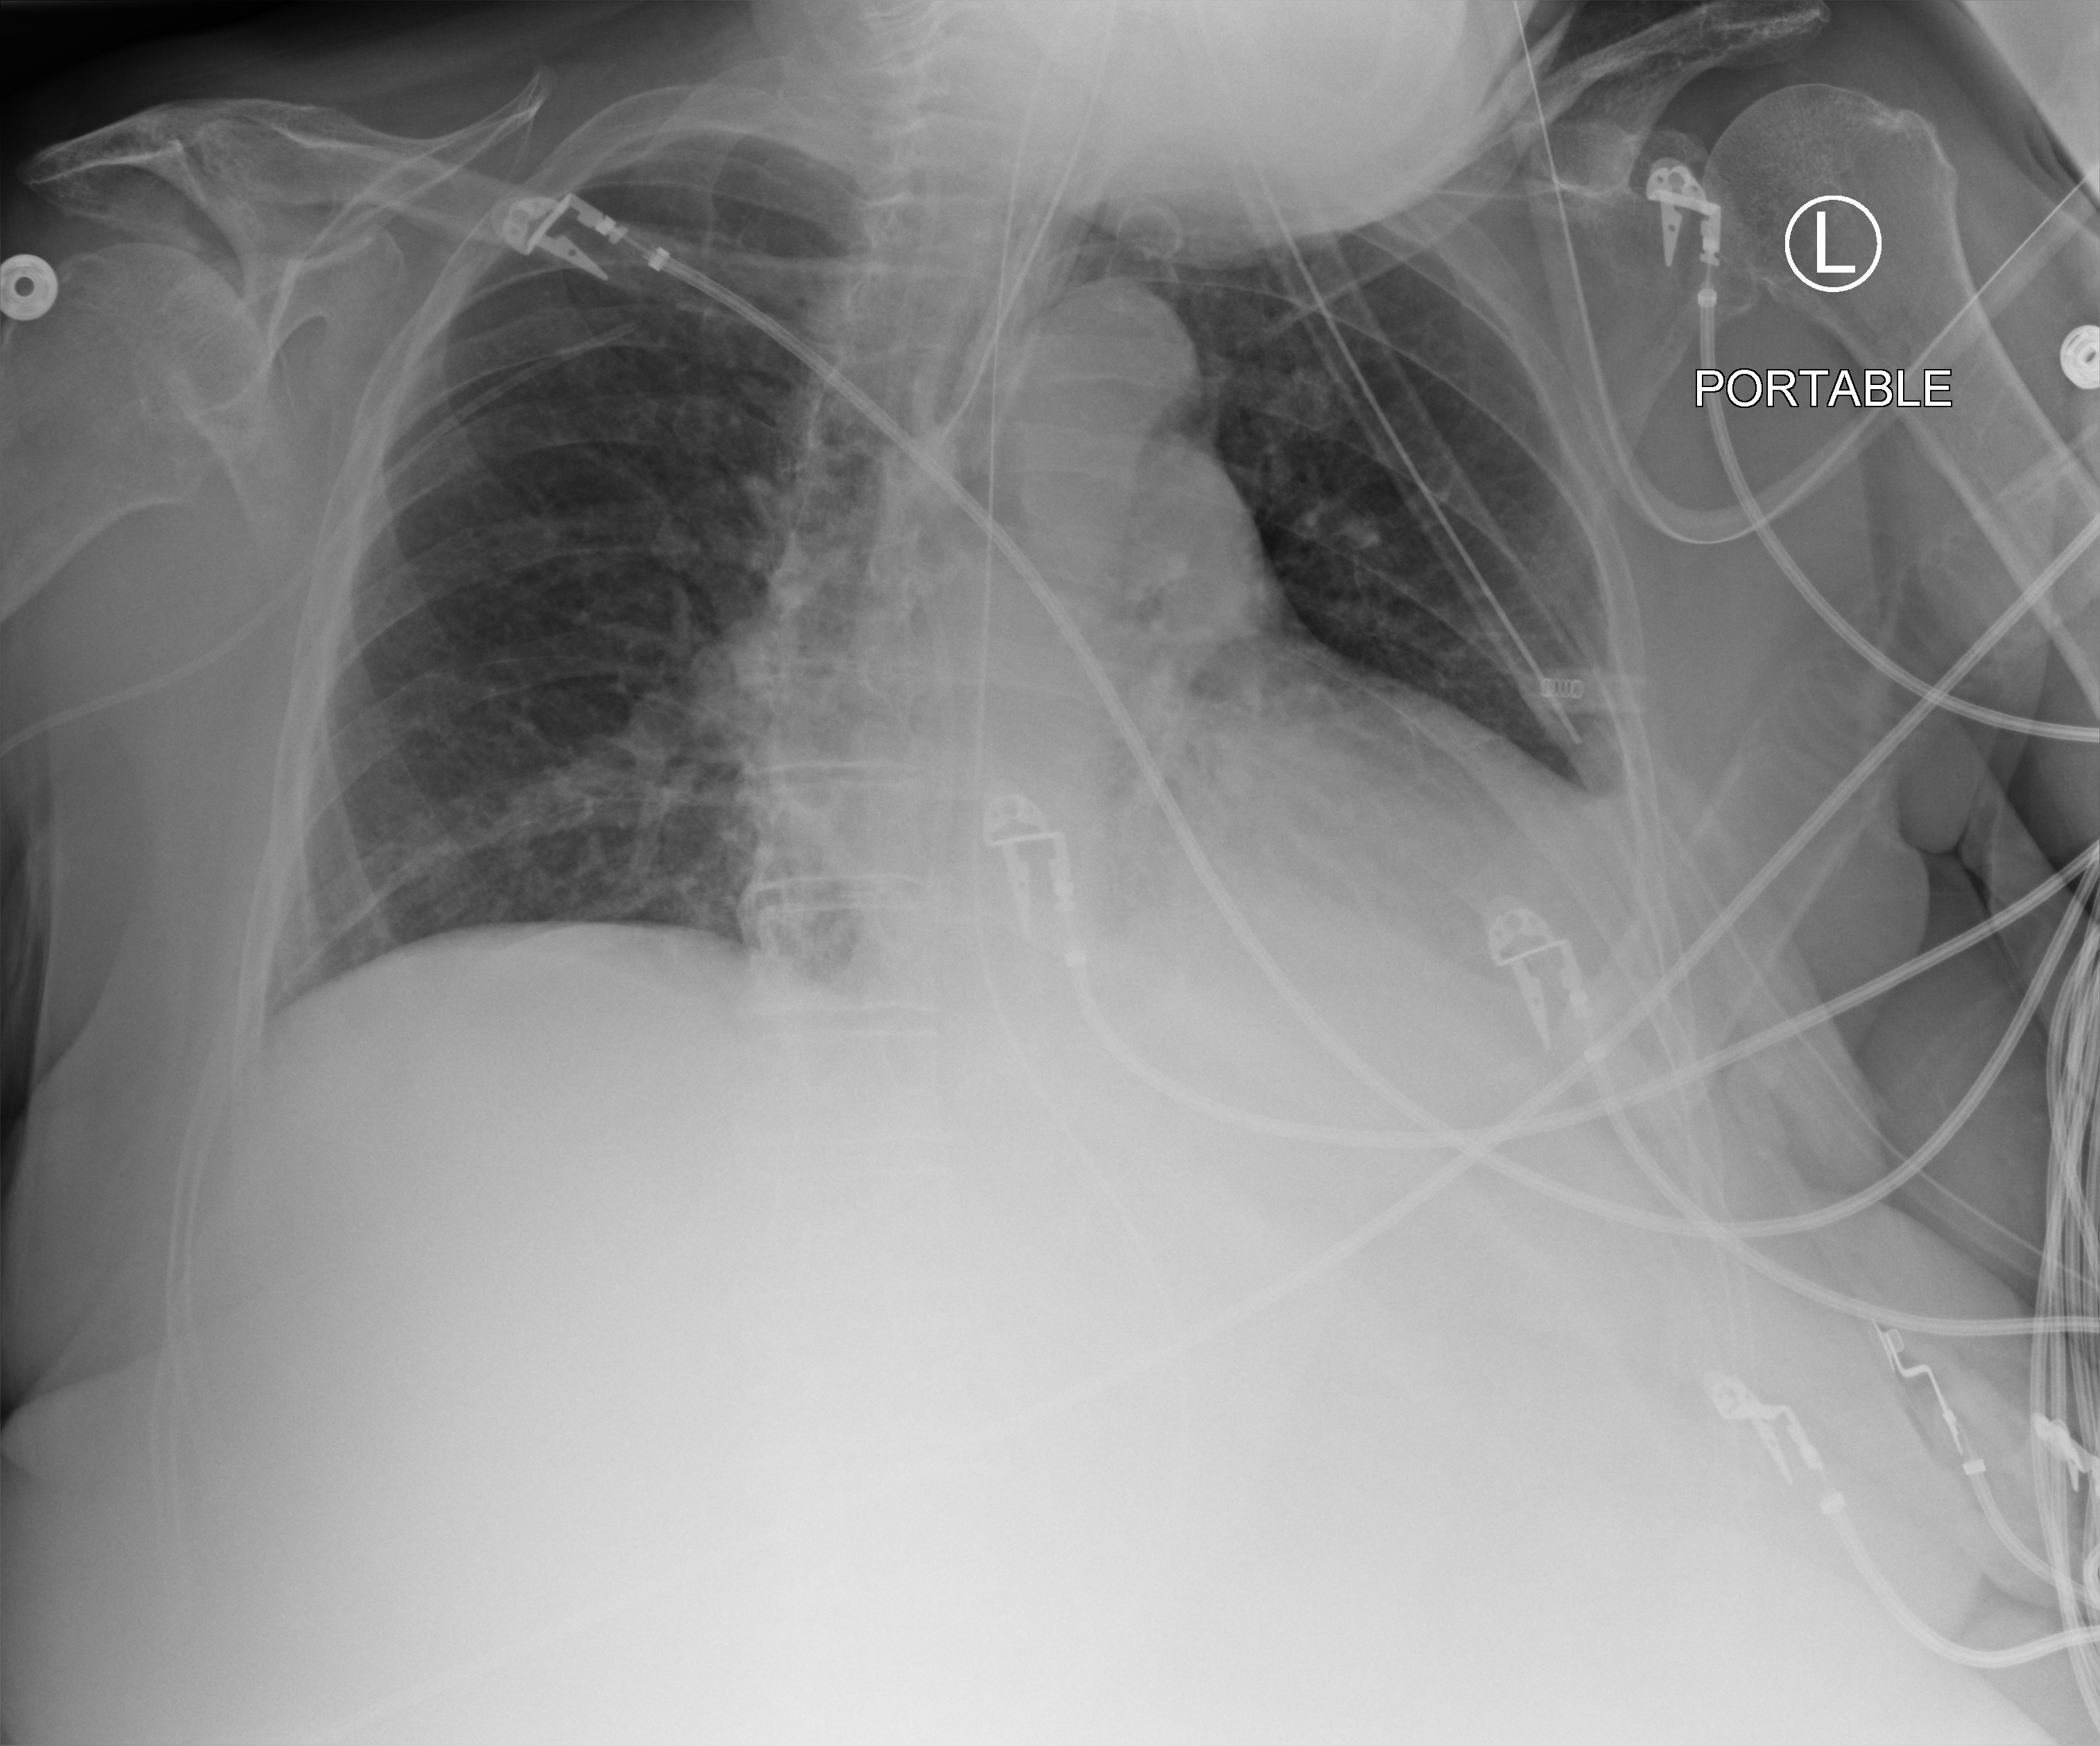
Portable chest radiograph; anteroposterior (AP) projection. Patient hospitalised with COVID-19; female, aged 75–90 years.
From the hospital-stay record, not from the radiograph (when in the stay this image was taken is not recorded):
- other chronic lung disease (admission record): no
- hypertension (admission record): yes